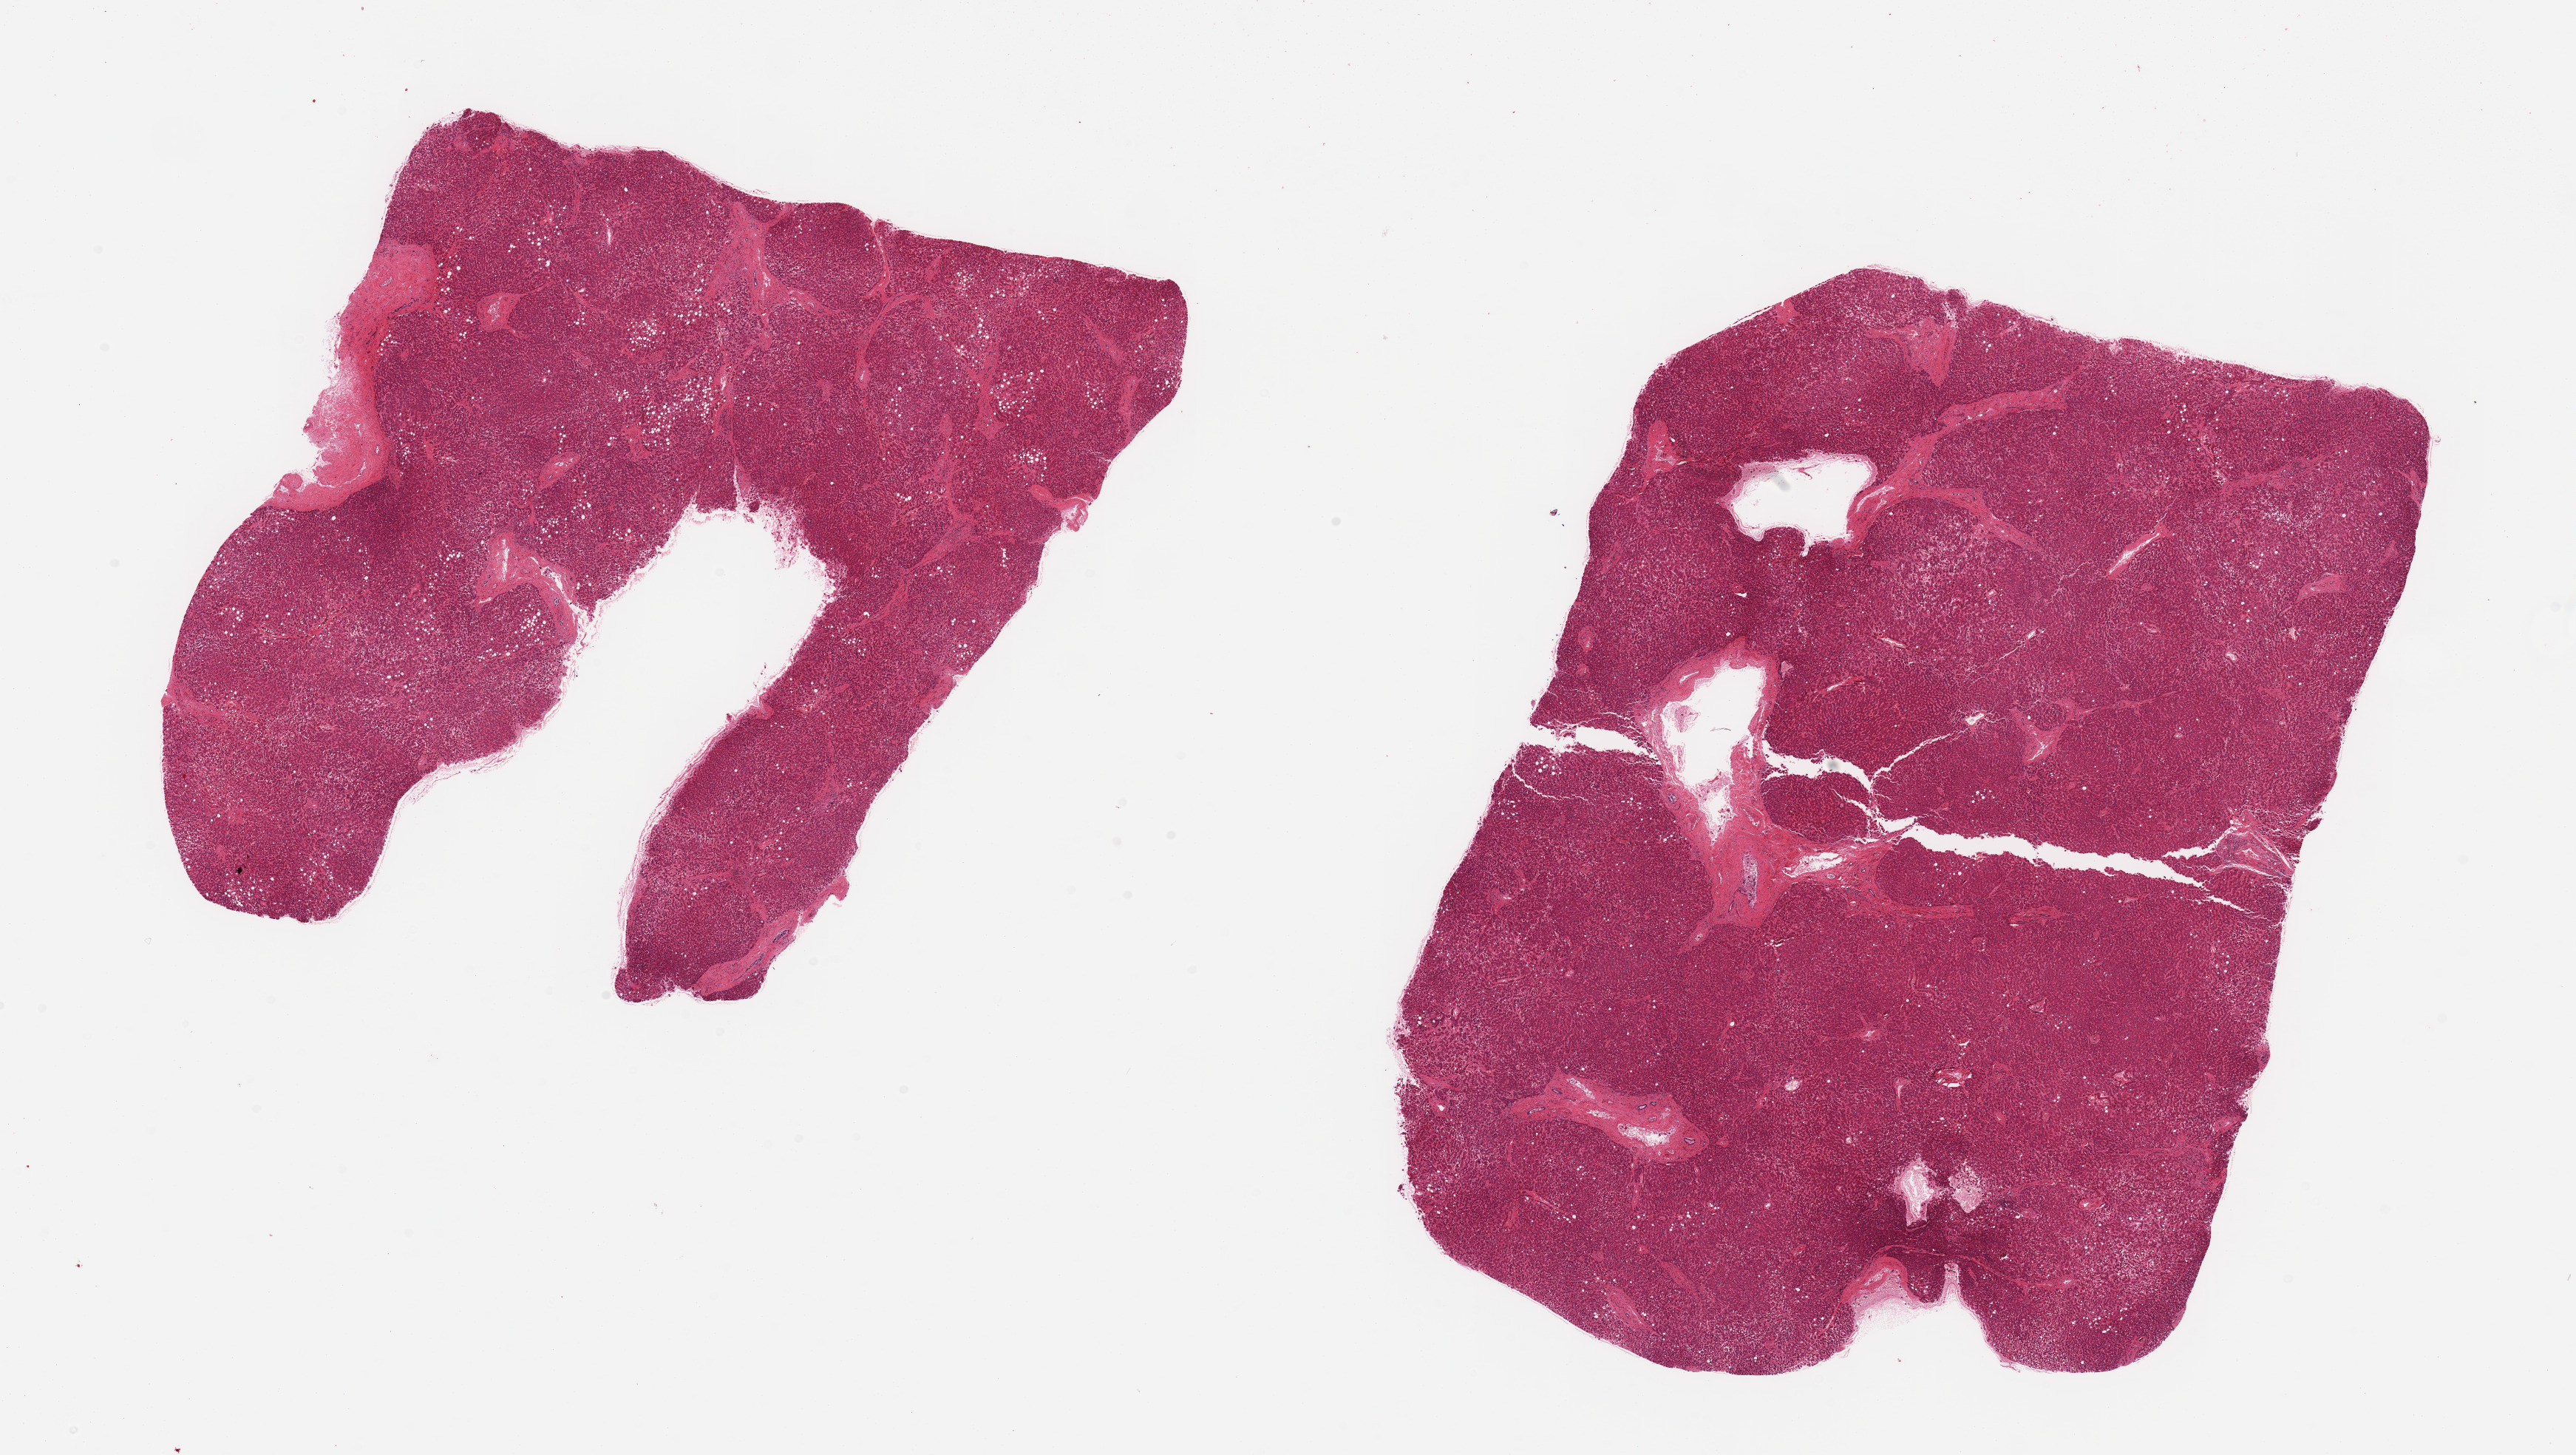
Hematoxylin and eosin (H&E) whole-slide image, brightfield, a low-resolution overview of the entire scanned area, about 27.6 x 15.6 mm; PAXgene-fixed paraffin-embedded (PFPE) section; target tissue: liver; tissue donor sample. Male donor.
Pathologist's review note for this sample: 2 pieces, macrovesicular steatosis in ~10% of parenchyma. Focal areas approach autolysis score 2.